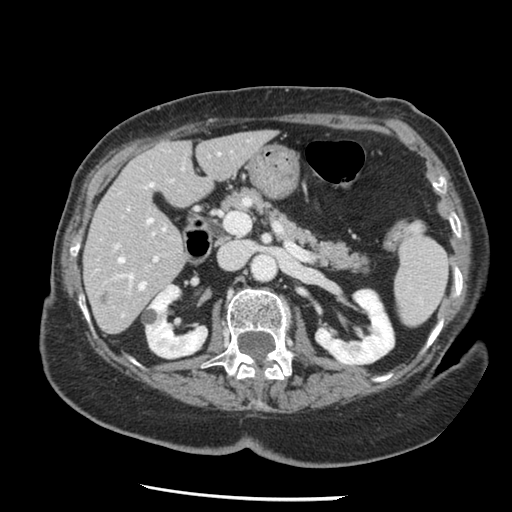
Contrast-enhanced abdominal CT, one axial slice. Slice 67 of 148 in the series (ordered by position). Reconstruction kernel STANDARD. 120 kVp. Intravenous contrast given. Soft-tissue window (W 400 / L 40 HU). 2.5 mm slice thickness. 512 × 512 image matrix, field of view 330 × 330 mm. Female patient, age 85 years. Case-level facts recorded for this patient, not image findings: diagnosis: colorectal cancer liver metastases, imaged before liver resection; multiple liver metastases: no; largest metastasis: 0.9 cm.
Outlined on this slice (expert manual segmentation):
- hepatic veins: bounding box <119,220,152,289> (left, top, right, bottom; pixels)
- liver: <84,132,273,333>
- planned liver remnant (the part of the liver to remain after resection): <84,132,273,325>
- portal vein (with intrahepatic branches): <116,208,159,284>
- liver metastasis: <100,293,110,304>